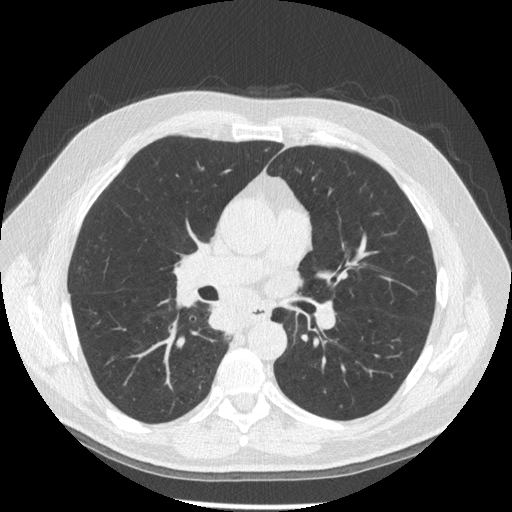
Low-dose screening chest CT, one axial slice; slice 102 of 181 in the series (ordered by position); reconstruction kernel STANDARD; lung window (W 1500 / L -600 HU); 512 × 512 image matrix, field of view 370 × 370 mm.
Annotated regions visible in this slice (outlined manually by an expert reader):
- lesion 1 (tumor, lower lobe of right lung): bounding box [x1, y1, x2, y2] px = [209, 304, 239, 336]